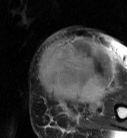
MRI of an extremity soft-tissue mass, one axial slice. Position 23 of 87 along the scan axis. T2-weighted fat-saturated. MR volume resampled by the dataset authors to the PET/CT grid (not the native acquisition matrix). 3.27 mm slice thickness. 127 × 138 image matrix, field of view 124 × 135 mm. Female patient. From the clinical record (not read from this slice): histological type: pleiomorphic leiomyosarcoma; grade: high; site of the primary tumour: left biceps.
Annotated regions visible in this slice (expert contour drawn on MRI and transferred to this co-registered scan by the dataset authors):
- gross tumour volume including surrounding oedema: box from (x=38, y=36) to (x=117, y=108) px
- gross tumour volume (mass): (x=38, y=36)–(x=117, y=104)